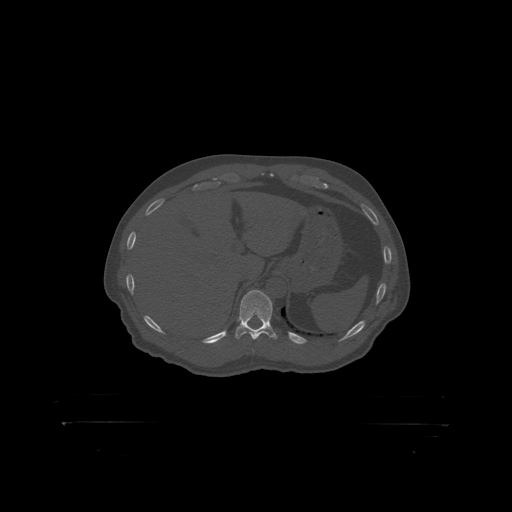
CT including the spine, one axial slice; position 379 of 399 along the scan axis; reconstruction kernel STANDARD; 120 kVp; bone window (W 1800 / L 400 HU); 512 × 512 image matrix. Male patient, age 46 years. From the clinical record (not read from this slice): primary cancer: skin.
Annotated regions visible in this slice (semi-automatic segmentation, software-assisted and operator-edited):
- T11 vertebra: box from (x=240, y=290) to (x=273, y=319) px